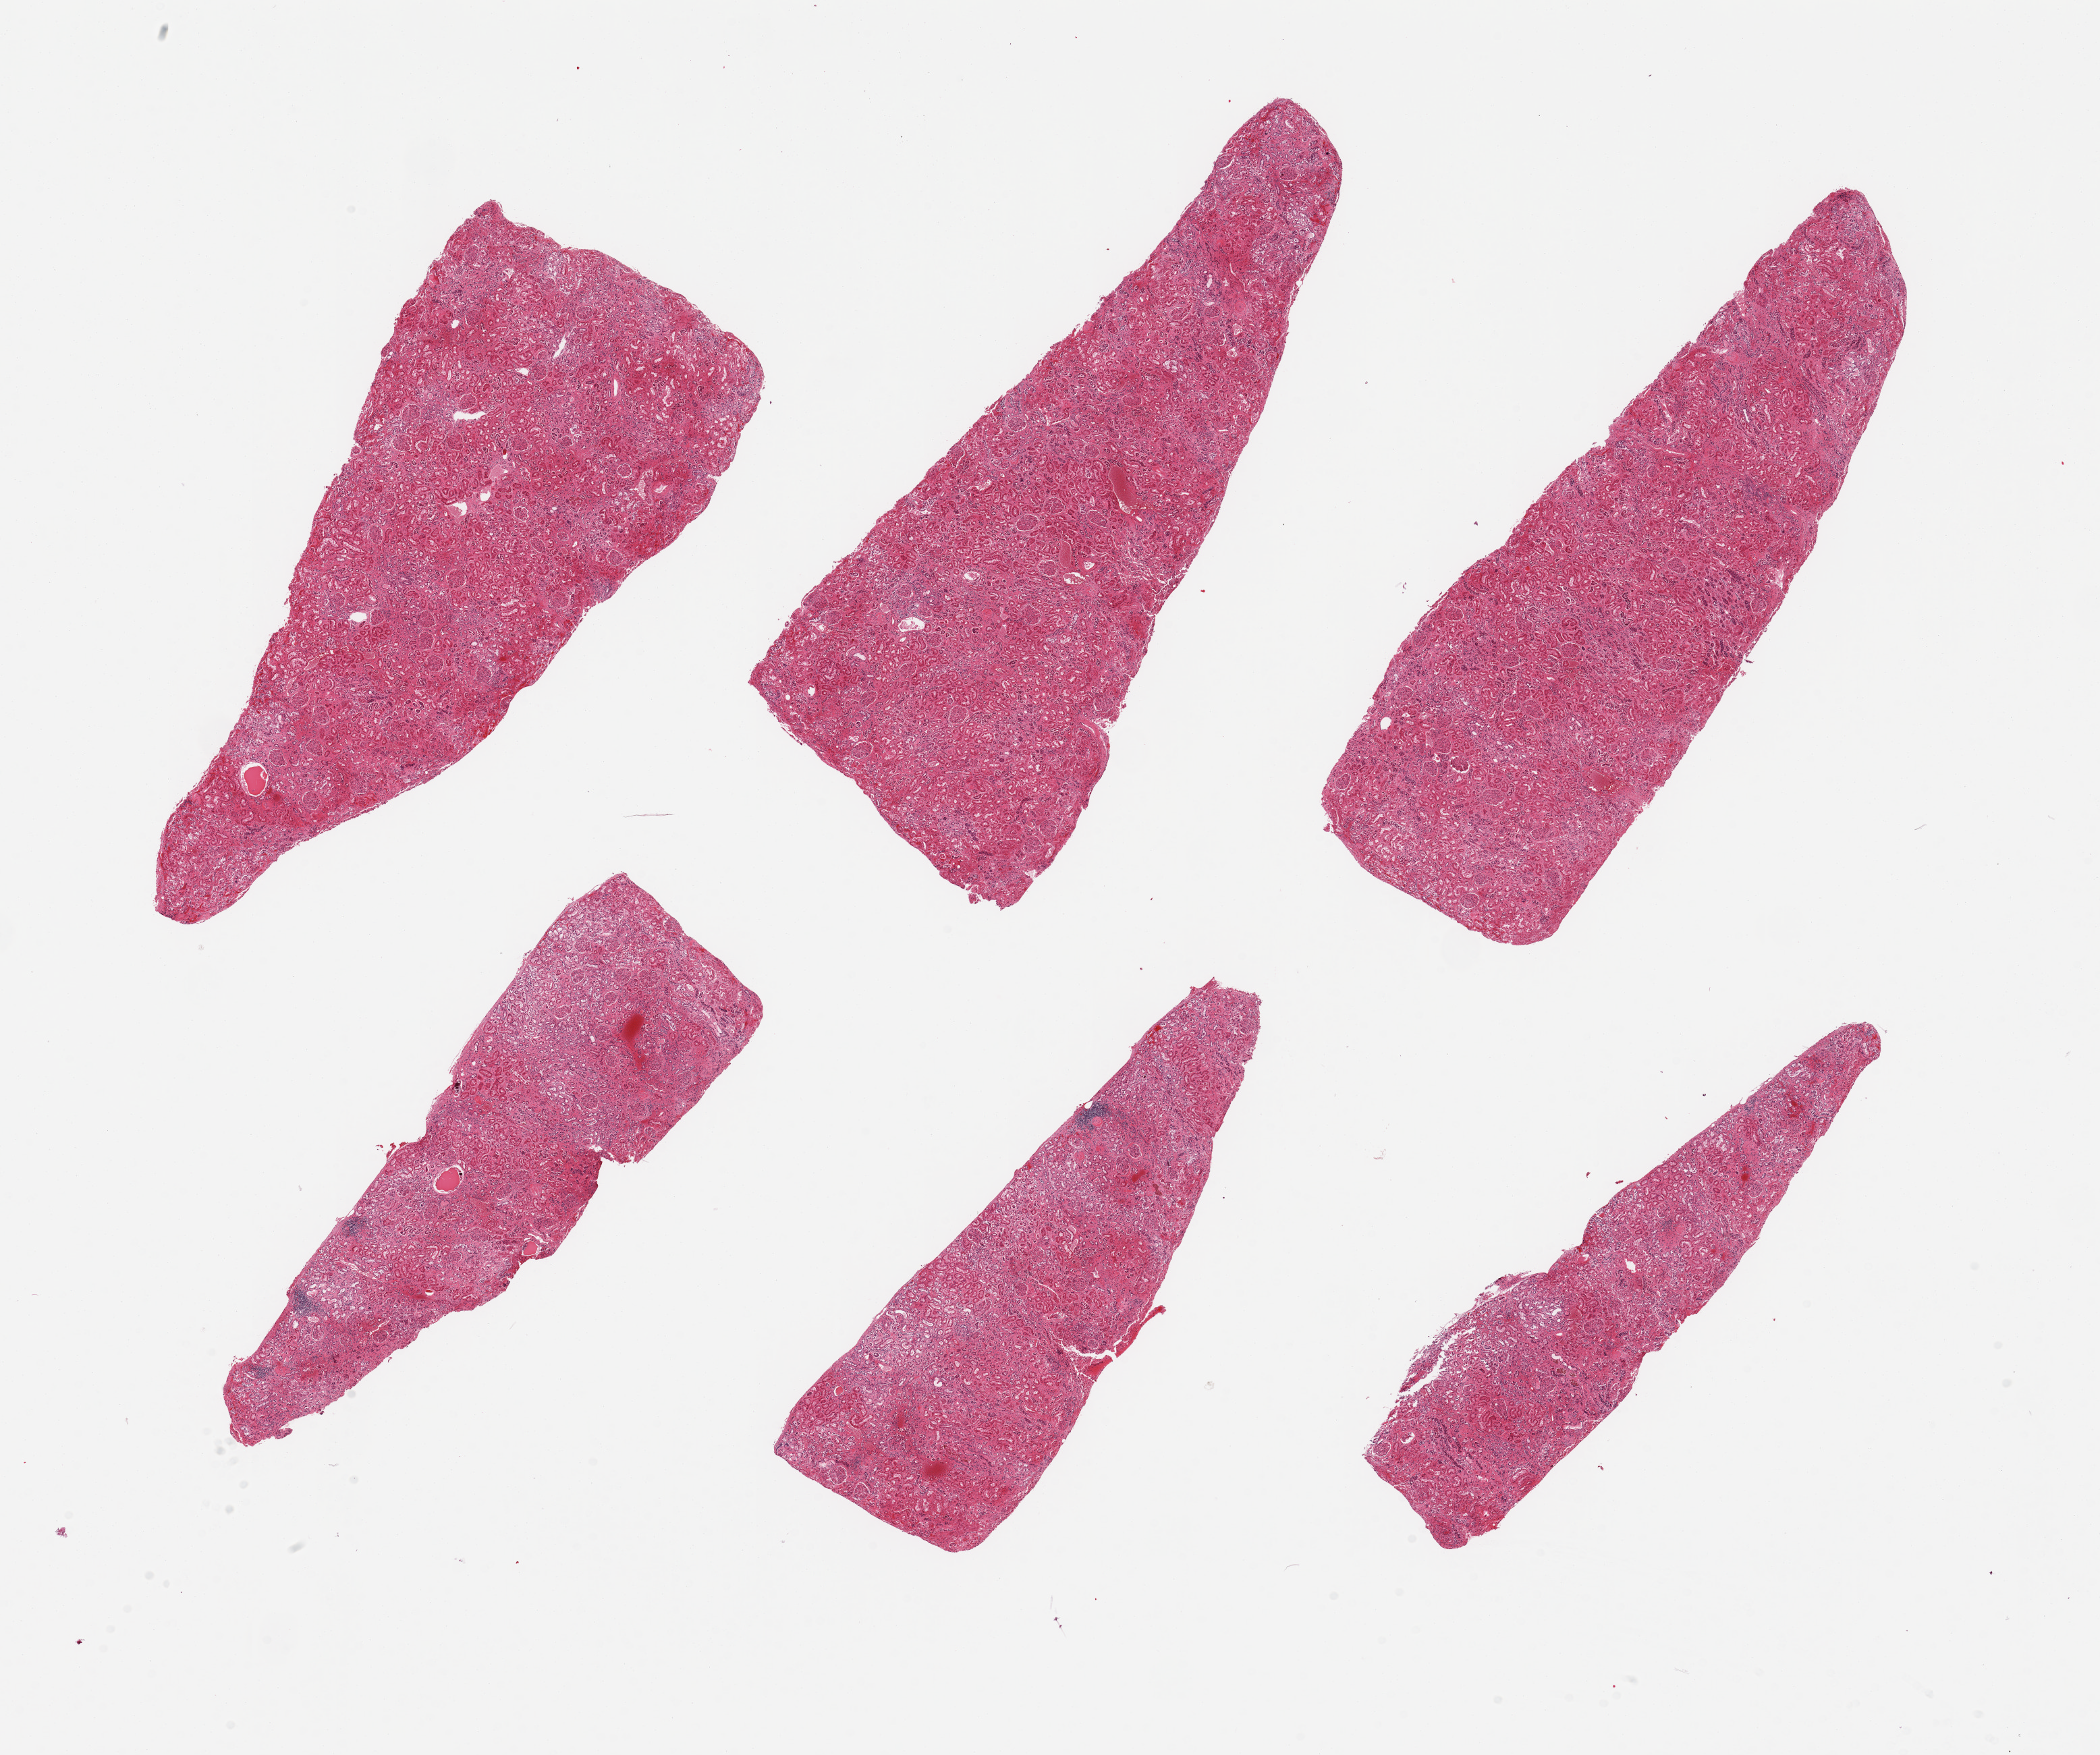
Digitized haematoxylin and eosin-stained section, brightfield — low-resolution overview of the scanned area, about 24.6 x 20.6 mm; PAXgene-fixed paraffin-embedded (PFPE) section; target tissue: renal cortex; tissue donor sample.
* review note (as recorded): 6 pieces, glomeruli present, moderate tubular autolysis